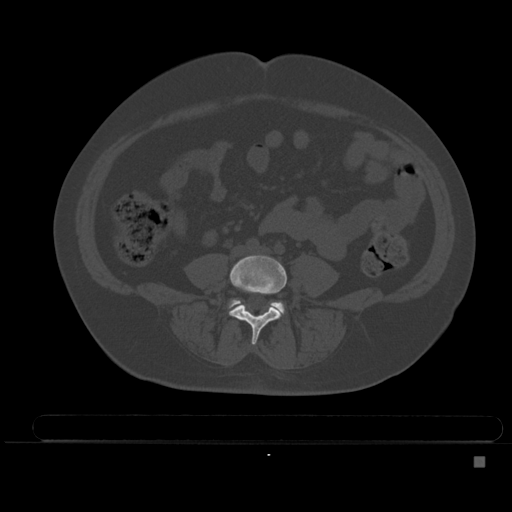
CT including the spine, one axial slice. Position 123 of 495 along the scan axis. Bone window (W 1800 / L 400 HU). 512 × 512 image matrix. Patient: female, 33 years. Case-level facts recorded for this patient, not image findings: primary cancer: breast; vertebrae with lytic lesions (as recorded): T1.
Annotated regions visible in this slice (semi-automatic segmentation, software-assisted and operator-edited):
- L4 vertebra: bounding box <229,255,287,345> (left, top, right, bottom; pixels)
- L5 vertebra: <231,300,284,314>